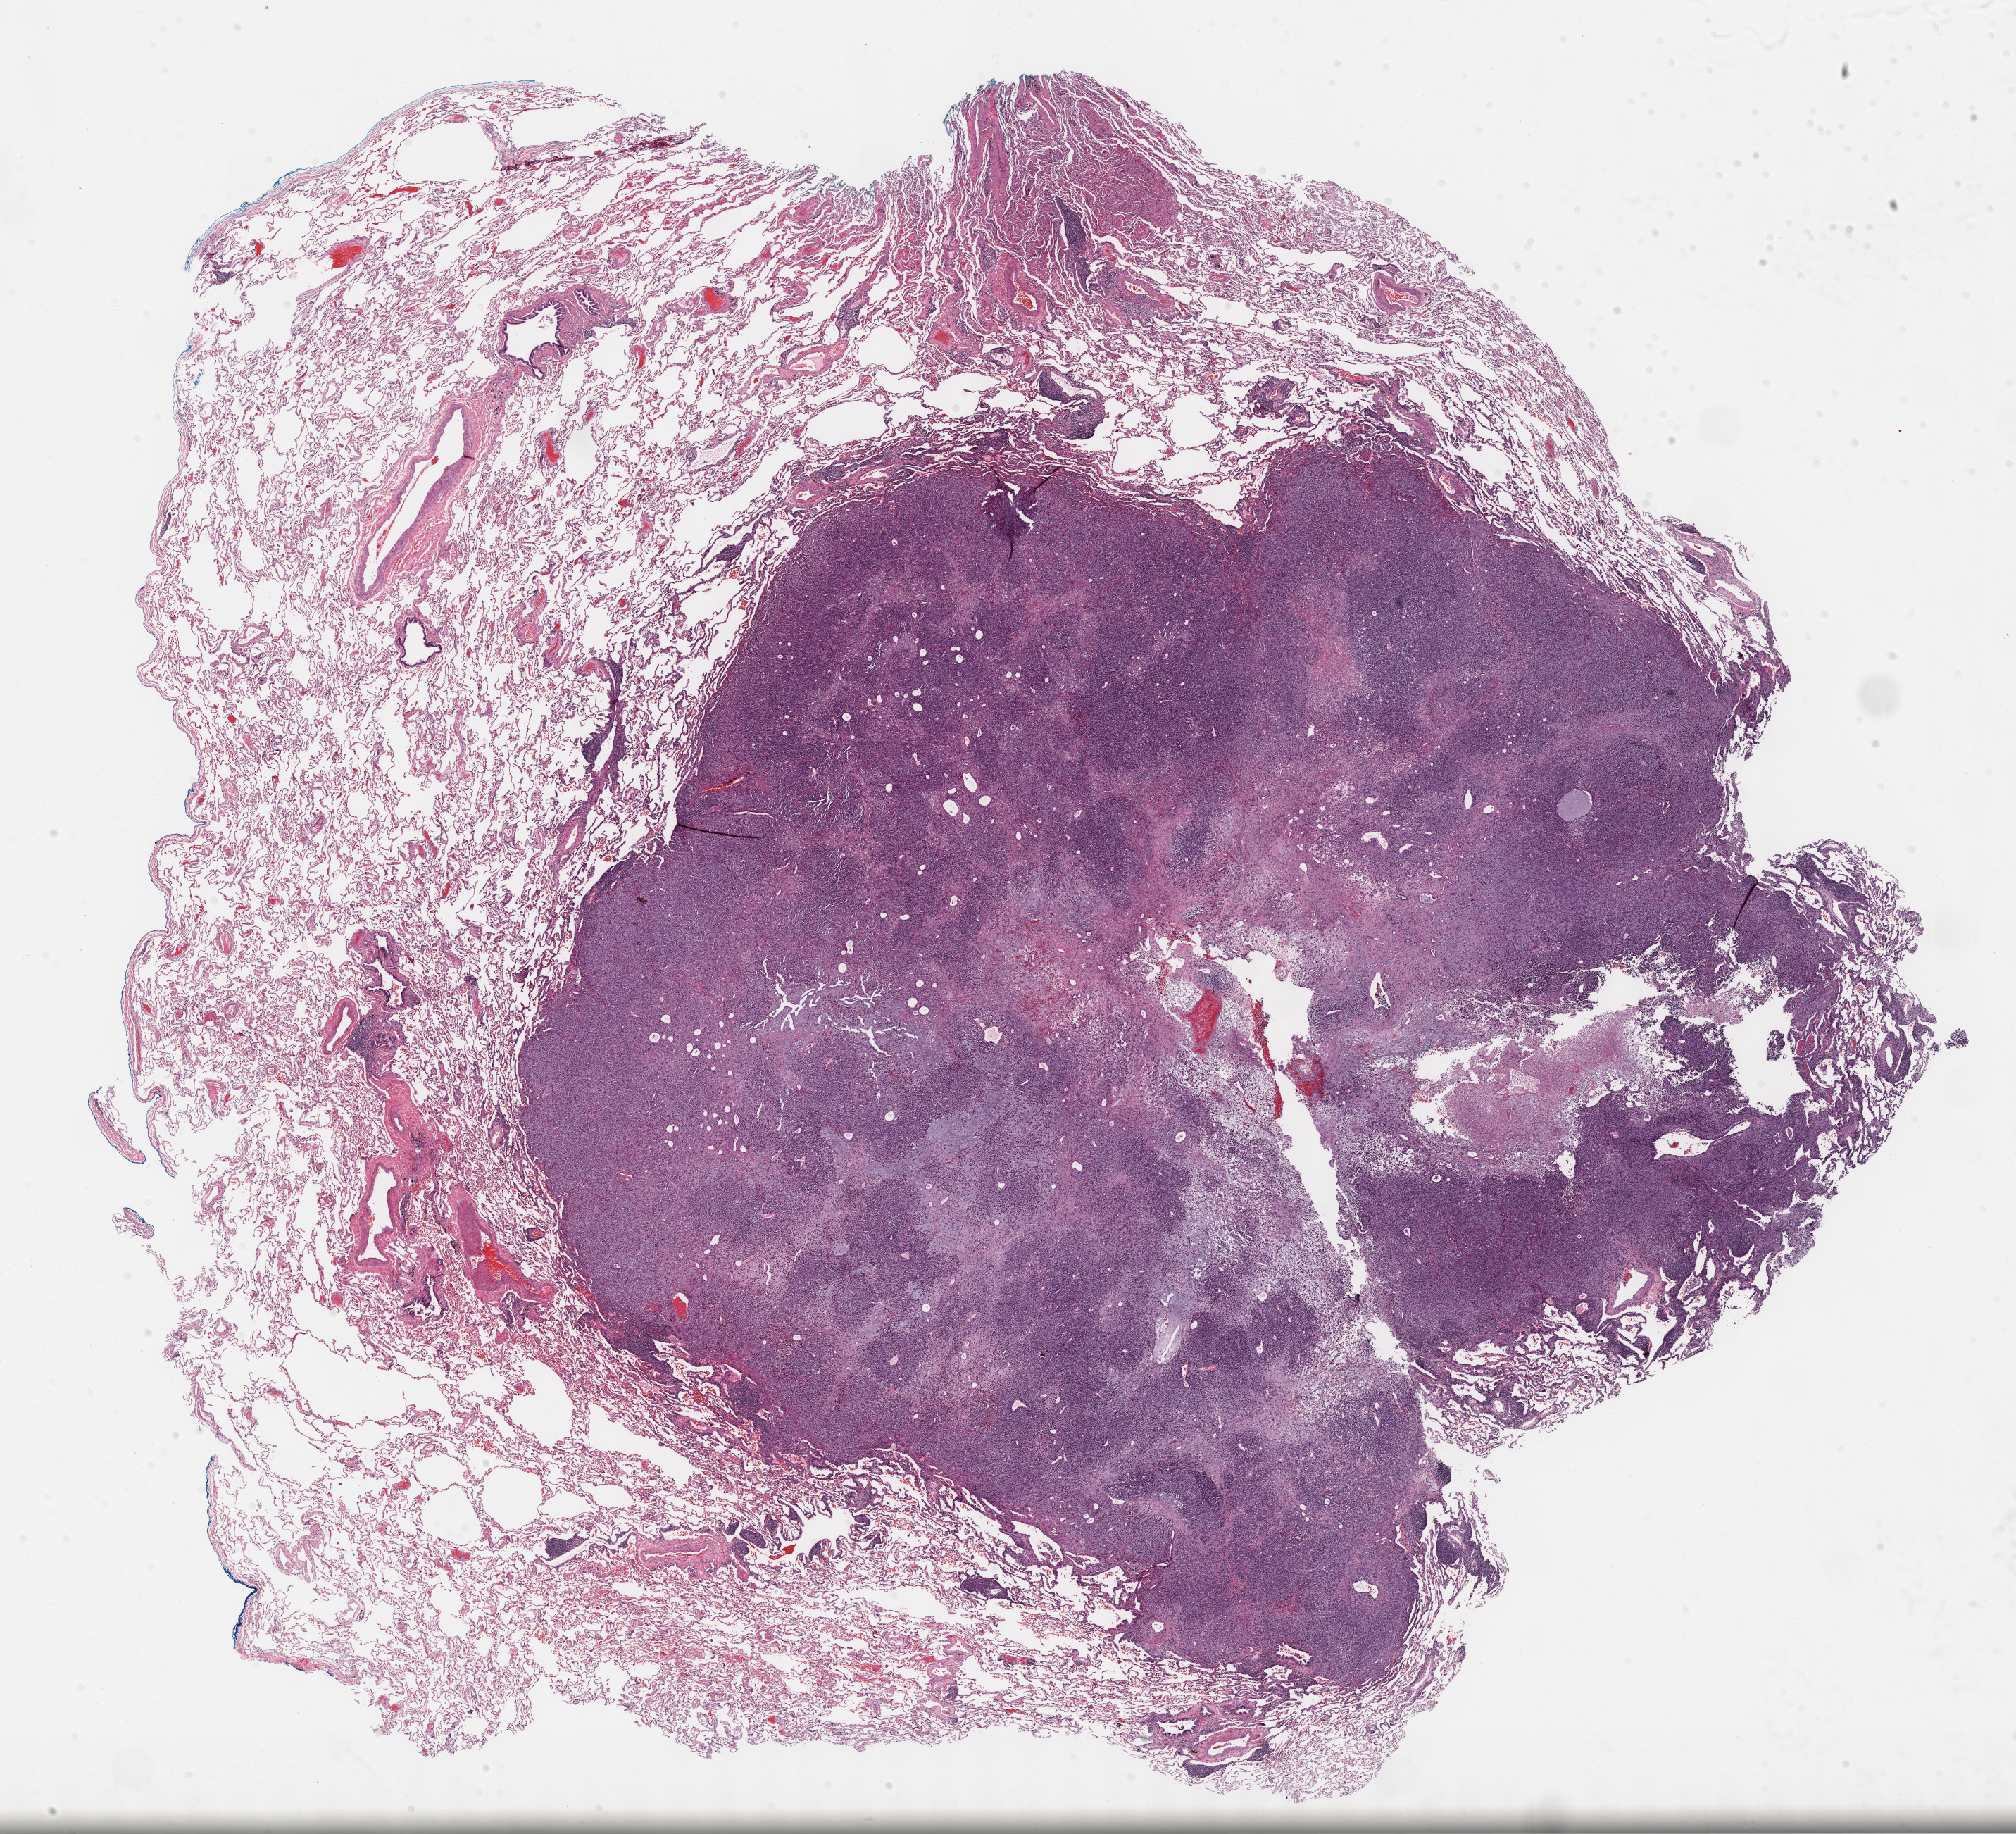
Hematoxylin and eosin (H&E) stained whole-slide image — whole scanned area (about 23.2 x 21.1 mm, acquisition: 40x scan) shown as a low-resolution overview; FFPE section; primary tumour sample from the skin. Patient: male, age at initial diagnosis 75 years.
Histologic diagnosis: Malignant melanoma, NOS.